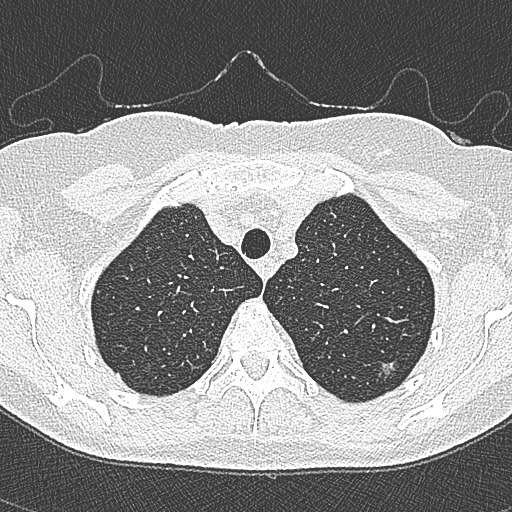
Chest CT (low-dose screening protocol), one axial image; second screening round (one year after baseline); lung window (W 1500 / L -600 HU); 512 × 512 image matrix, field of view 298 × 298 mm. Female, age 65 years at enrolment. Current smoker at enrolment.
Lesion marked by an expert reader, bounding box (x1, y1, x2, y2) in pixels: (367, 347, 410, 388). The screening reader recorded 4 non-calcified nodules or masses ≥4 mm on this exam (left upper lobe, left upper lobe, left upper lobe, right lower lobe); which of them this box marks is not recorded.